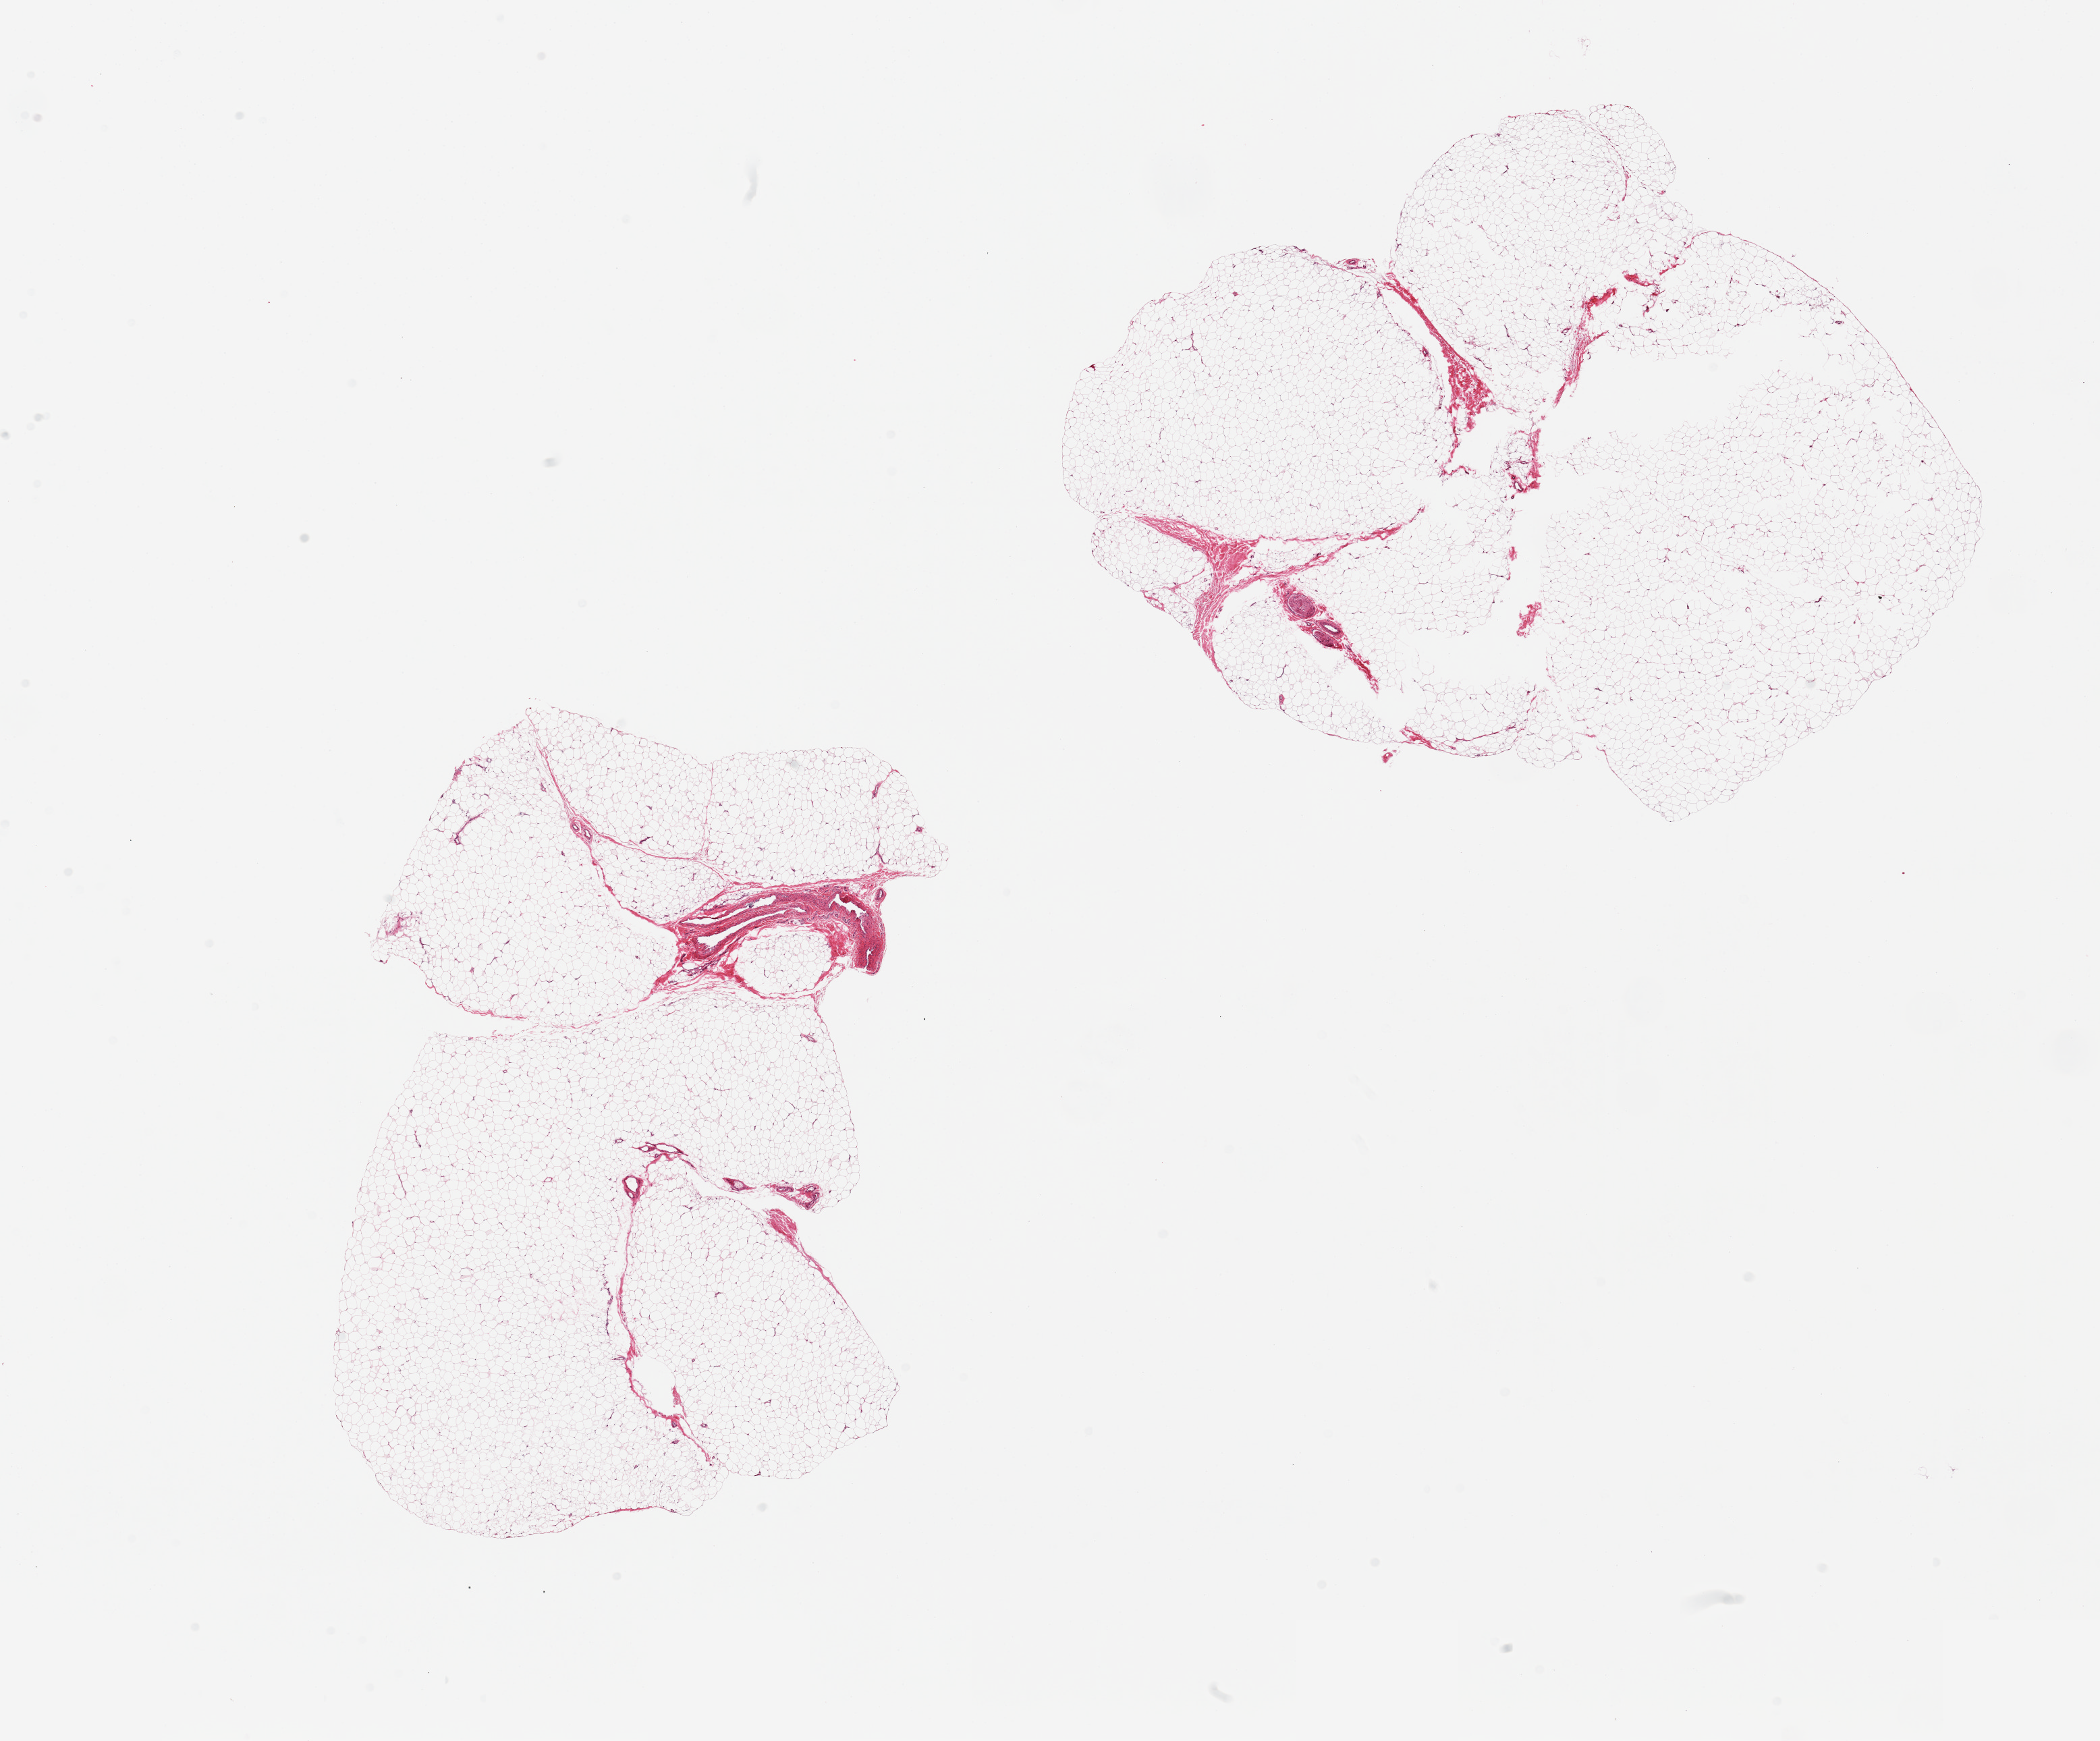
Whole-slide image, H&E stain, a low-resolution overview of the entire scanned area, about 24.6 x 20.4 mm (acquisition: 20x scan); PAXgene-fixed, paraffin-embedded tissue; section of adipose tissue (target tissue); donor tissue sample.
Review note (as recorded): 2 pieces; includes small portion of fibrovascular tissue and nerve.